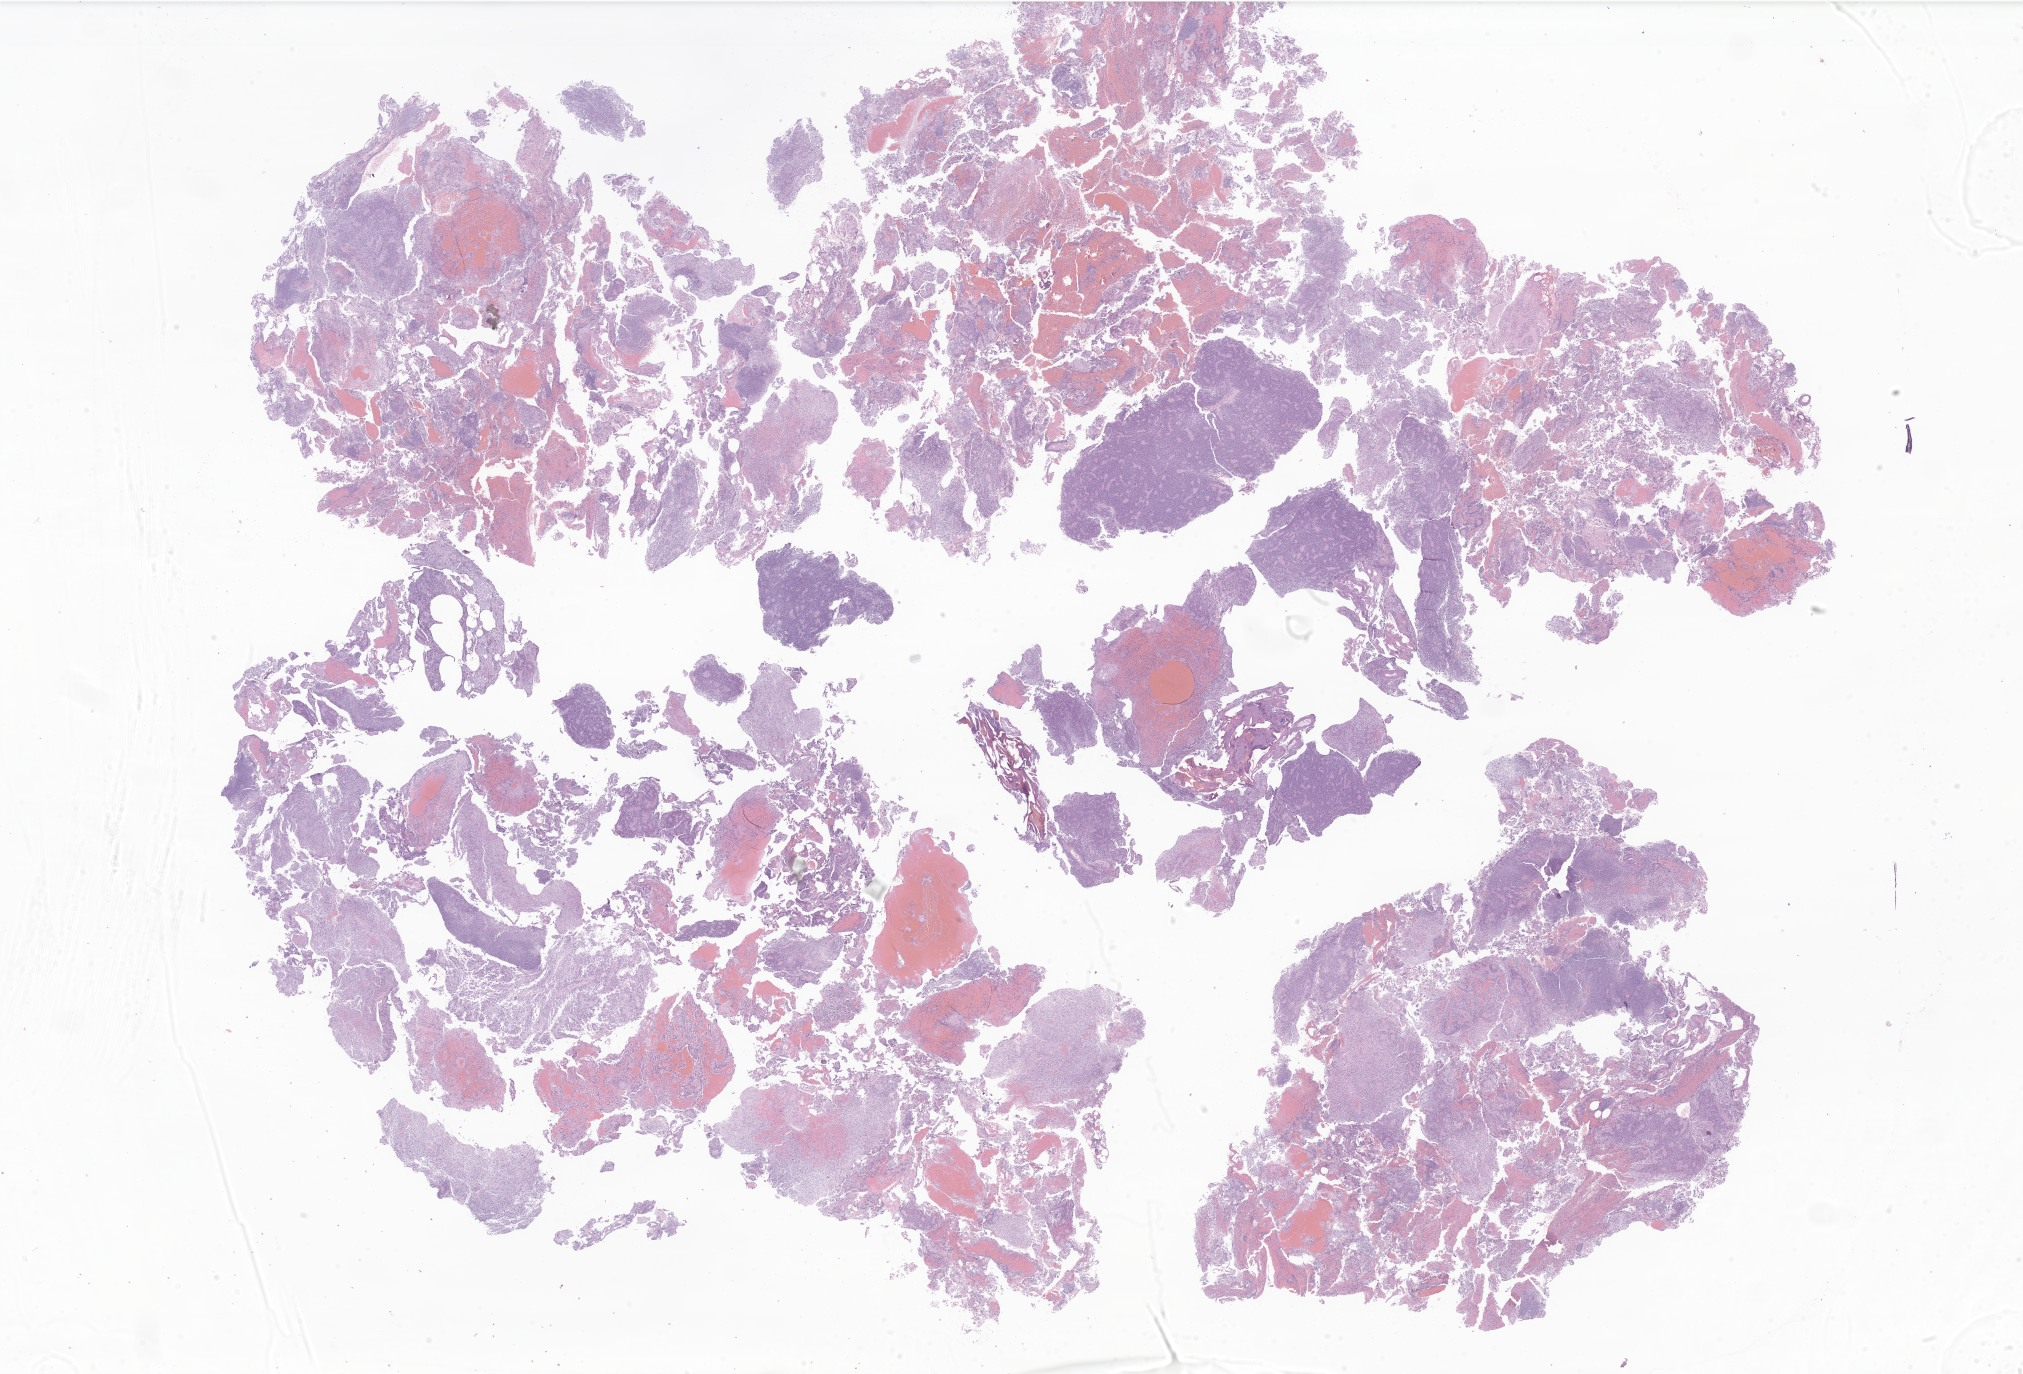
Digitized hematoxylin and eosin (H&E)-stained section of tumor tissue from the brain, low-resolution overview of the scanned area, about 34.1 x 23.2 mm. Formalin-fixed paraffin-embedded section. Patient female; age 57 months (4 years 9 months).
Diagnosis (ICD-O-3 morphology term): Ependymoma, NOS.